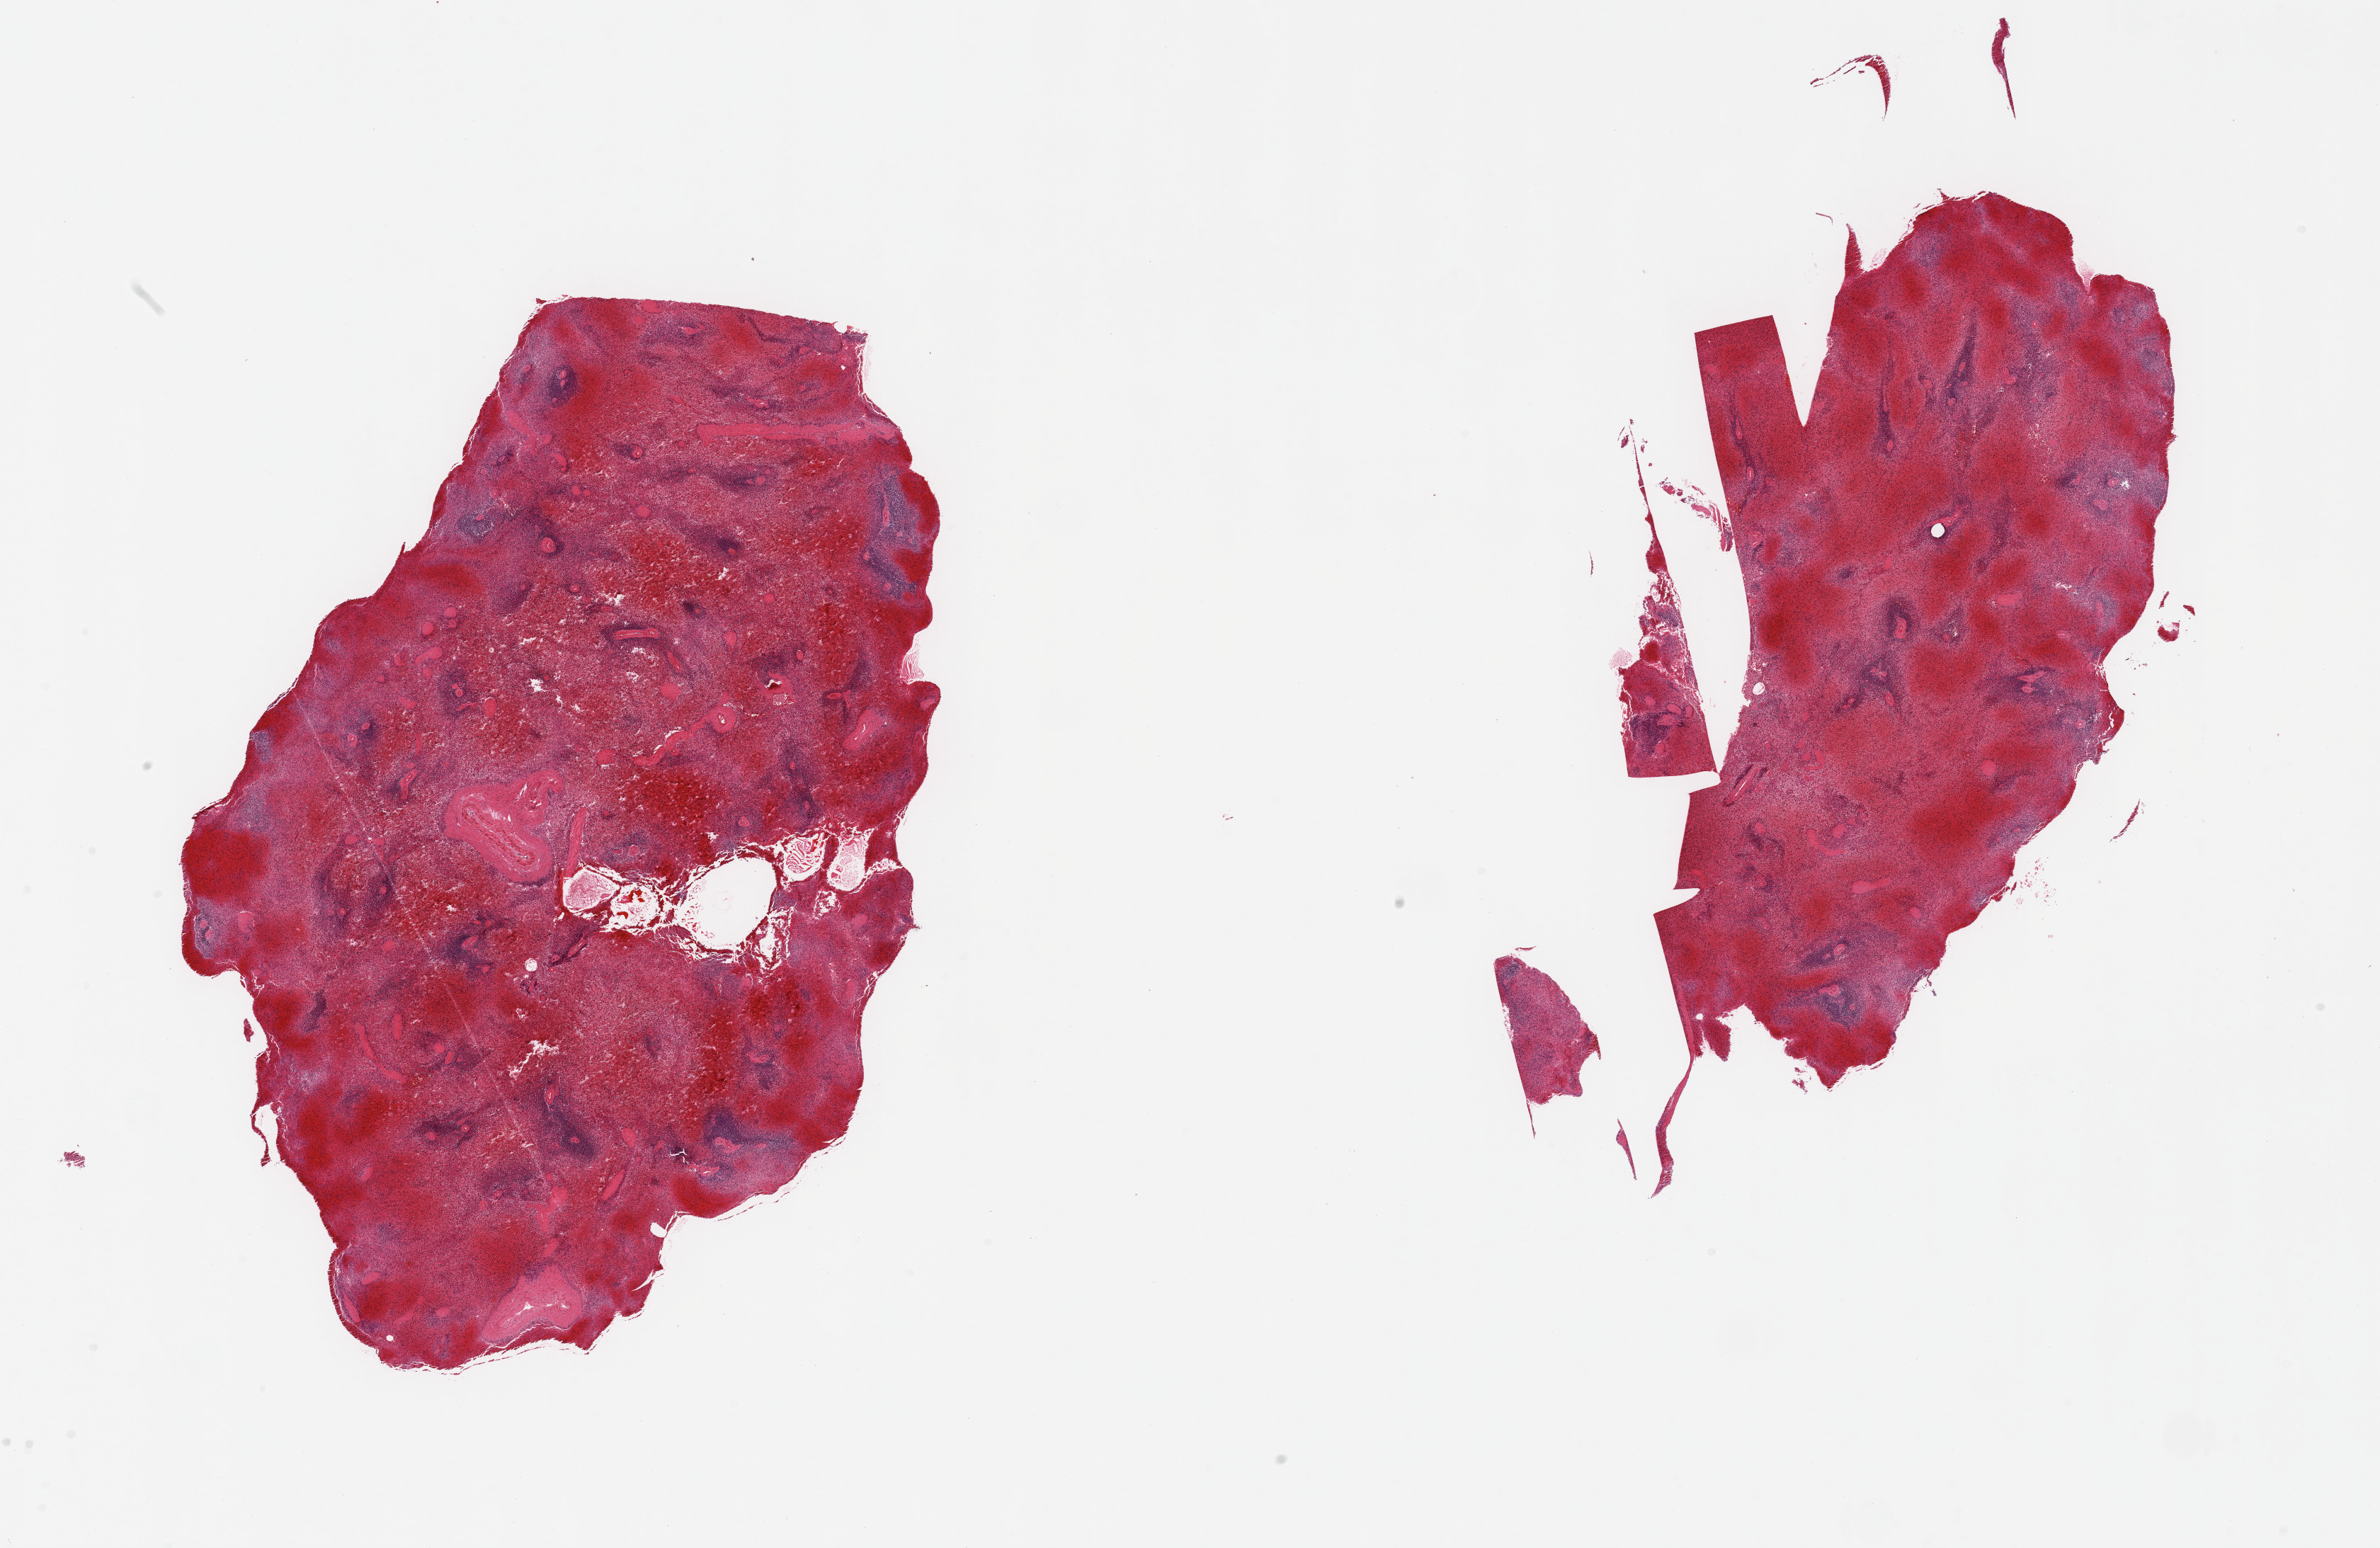
Digitized hematoxylin and eosin (H&E)-stained section, shown as a low-resolution overview of the whole scanned area (about 26.6 x 17.3 mm, slide scanned at 20x). PAXgene-fixed, paraffin-embedded tissue. Section of spleen (target tissue). Donor tissue sample.
Review note (as recorded): 2 pieces, moderate congestion.